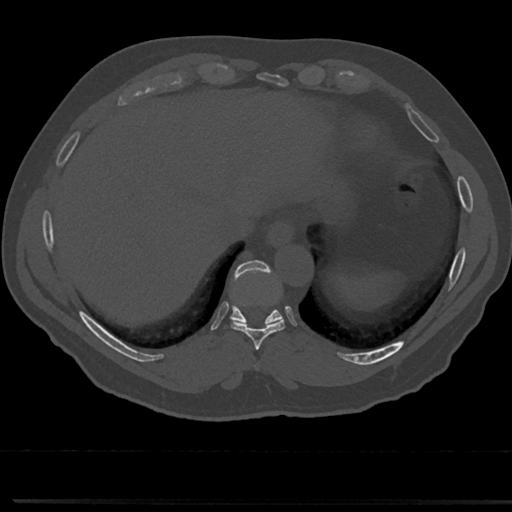
CT including the spine, one axial slice. Position 288 of 817 along the scan axis. Reconstruction kernel Br40s/3. Bone window (W 1800 / L 400 HU). 0.5 mm slice thickness. 512 × 512 image matrix. Male patient, age 61 years. From the clinical record (not read from this slice): primary cancer: prostate.
Structures marked on this image (semi-automatic segmentation, software-assisted and operator-edited):
- T8 vertebra: bounding box <255,344,263,372> (left, top, right, bottom; pixels)
- T9 vertebra: <211,264,303,350>